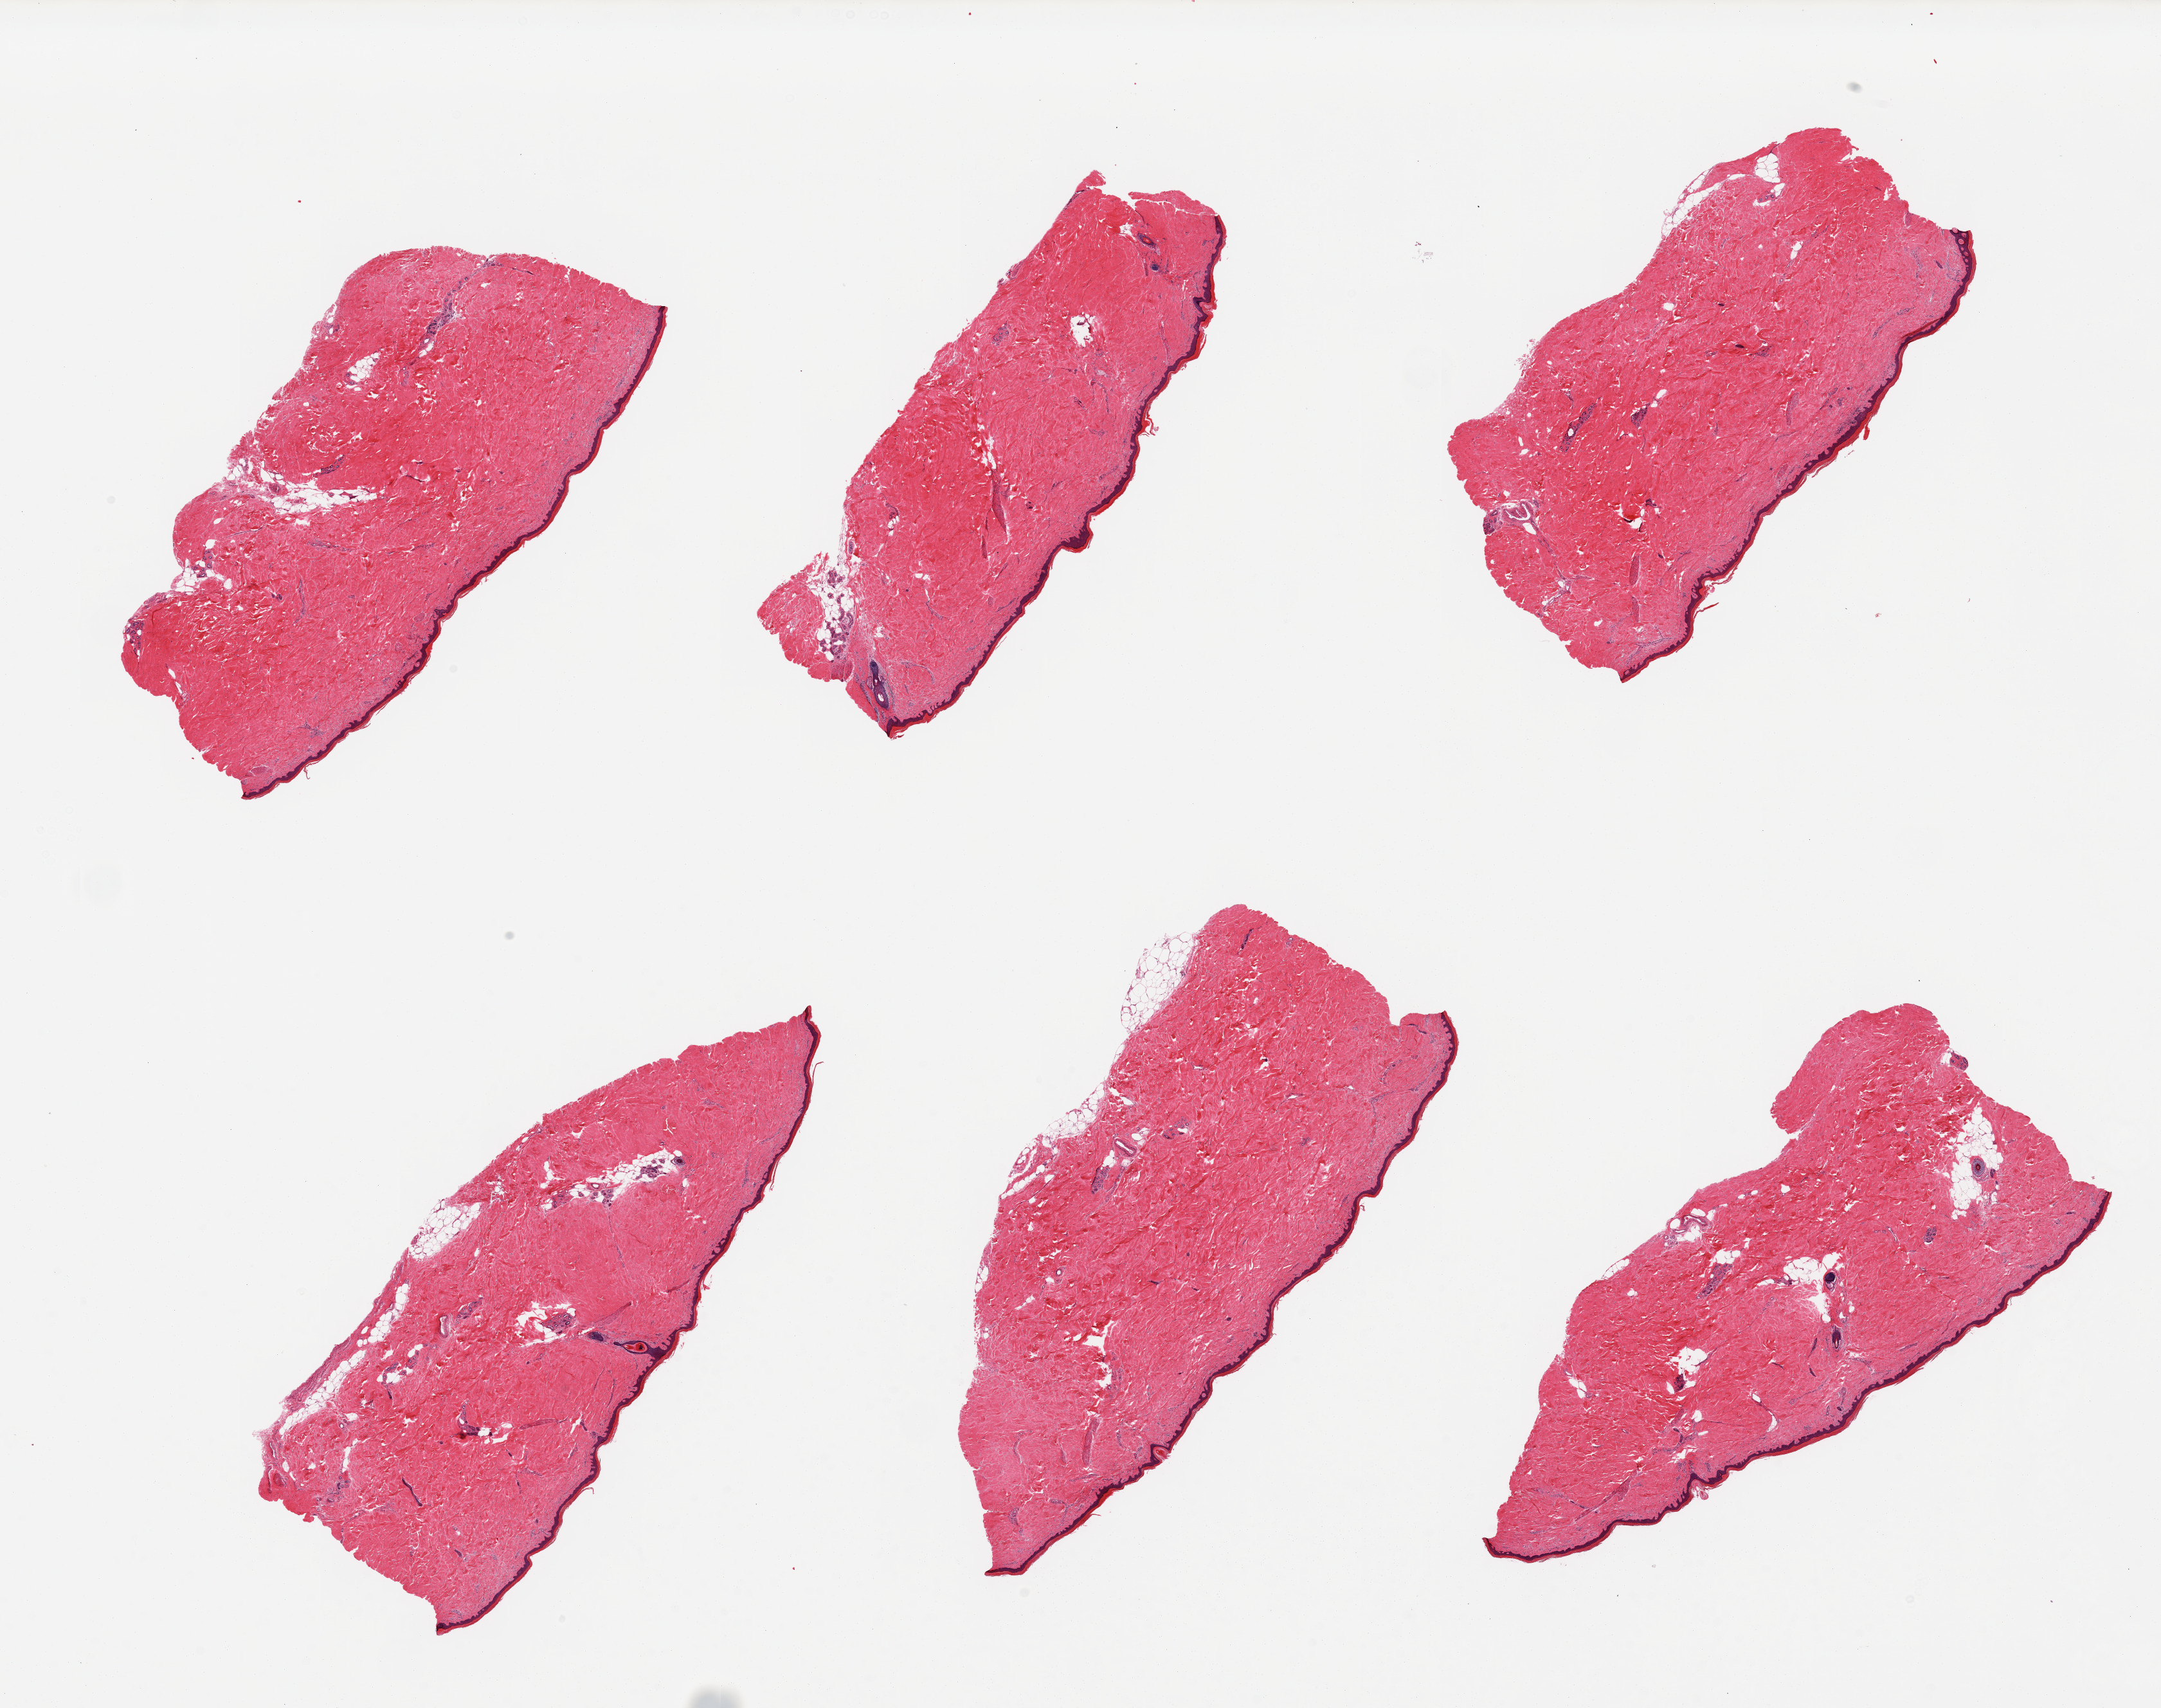
Digitized haematoxylin and eosin-stained section, brightfield, low-resolution overview of the scanned area, about 26.6 x 21.0 mm (from a 20x scan). PAXgene-fixed, paraffin-embedded tissue. Target tissue: skin of lower leg. Tissue donor sample. Female donor.
Review note (as recorded): 6 pieces, well trimmed, squamous epithelium measures up to 83 microns.